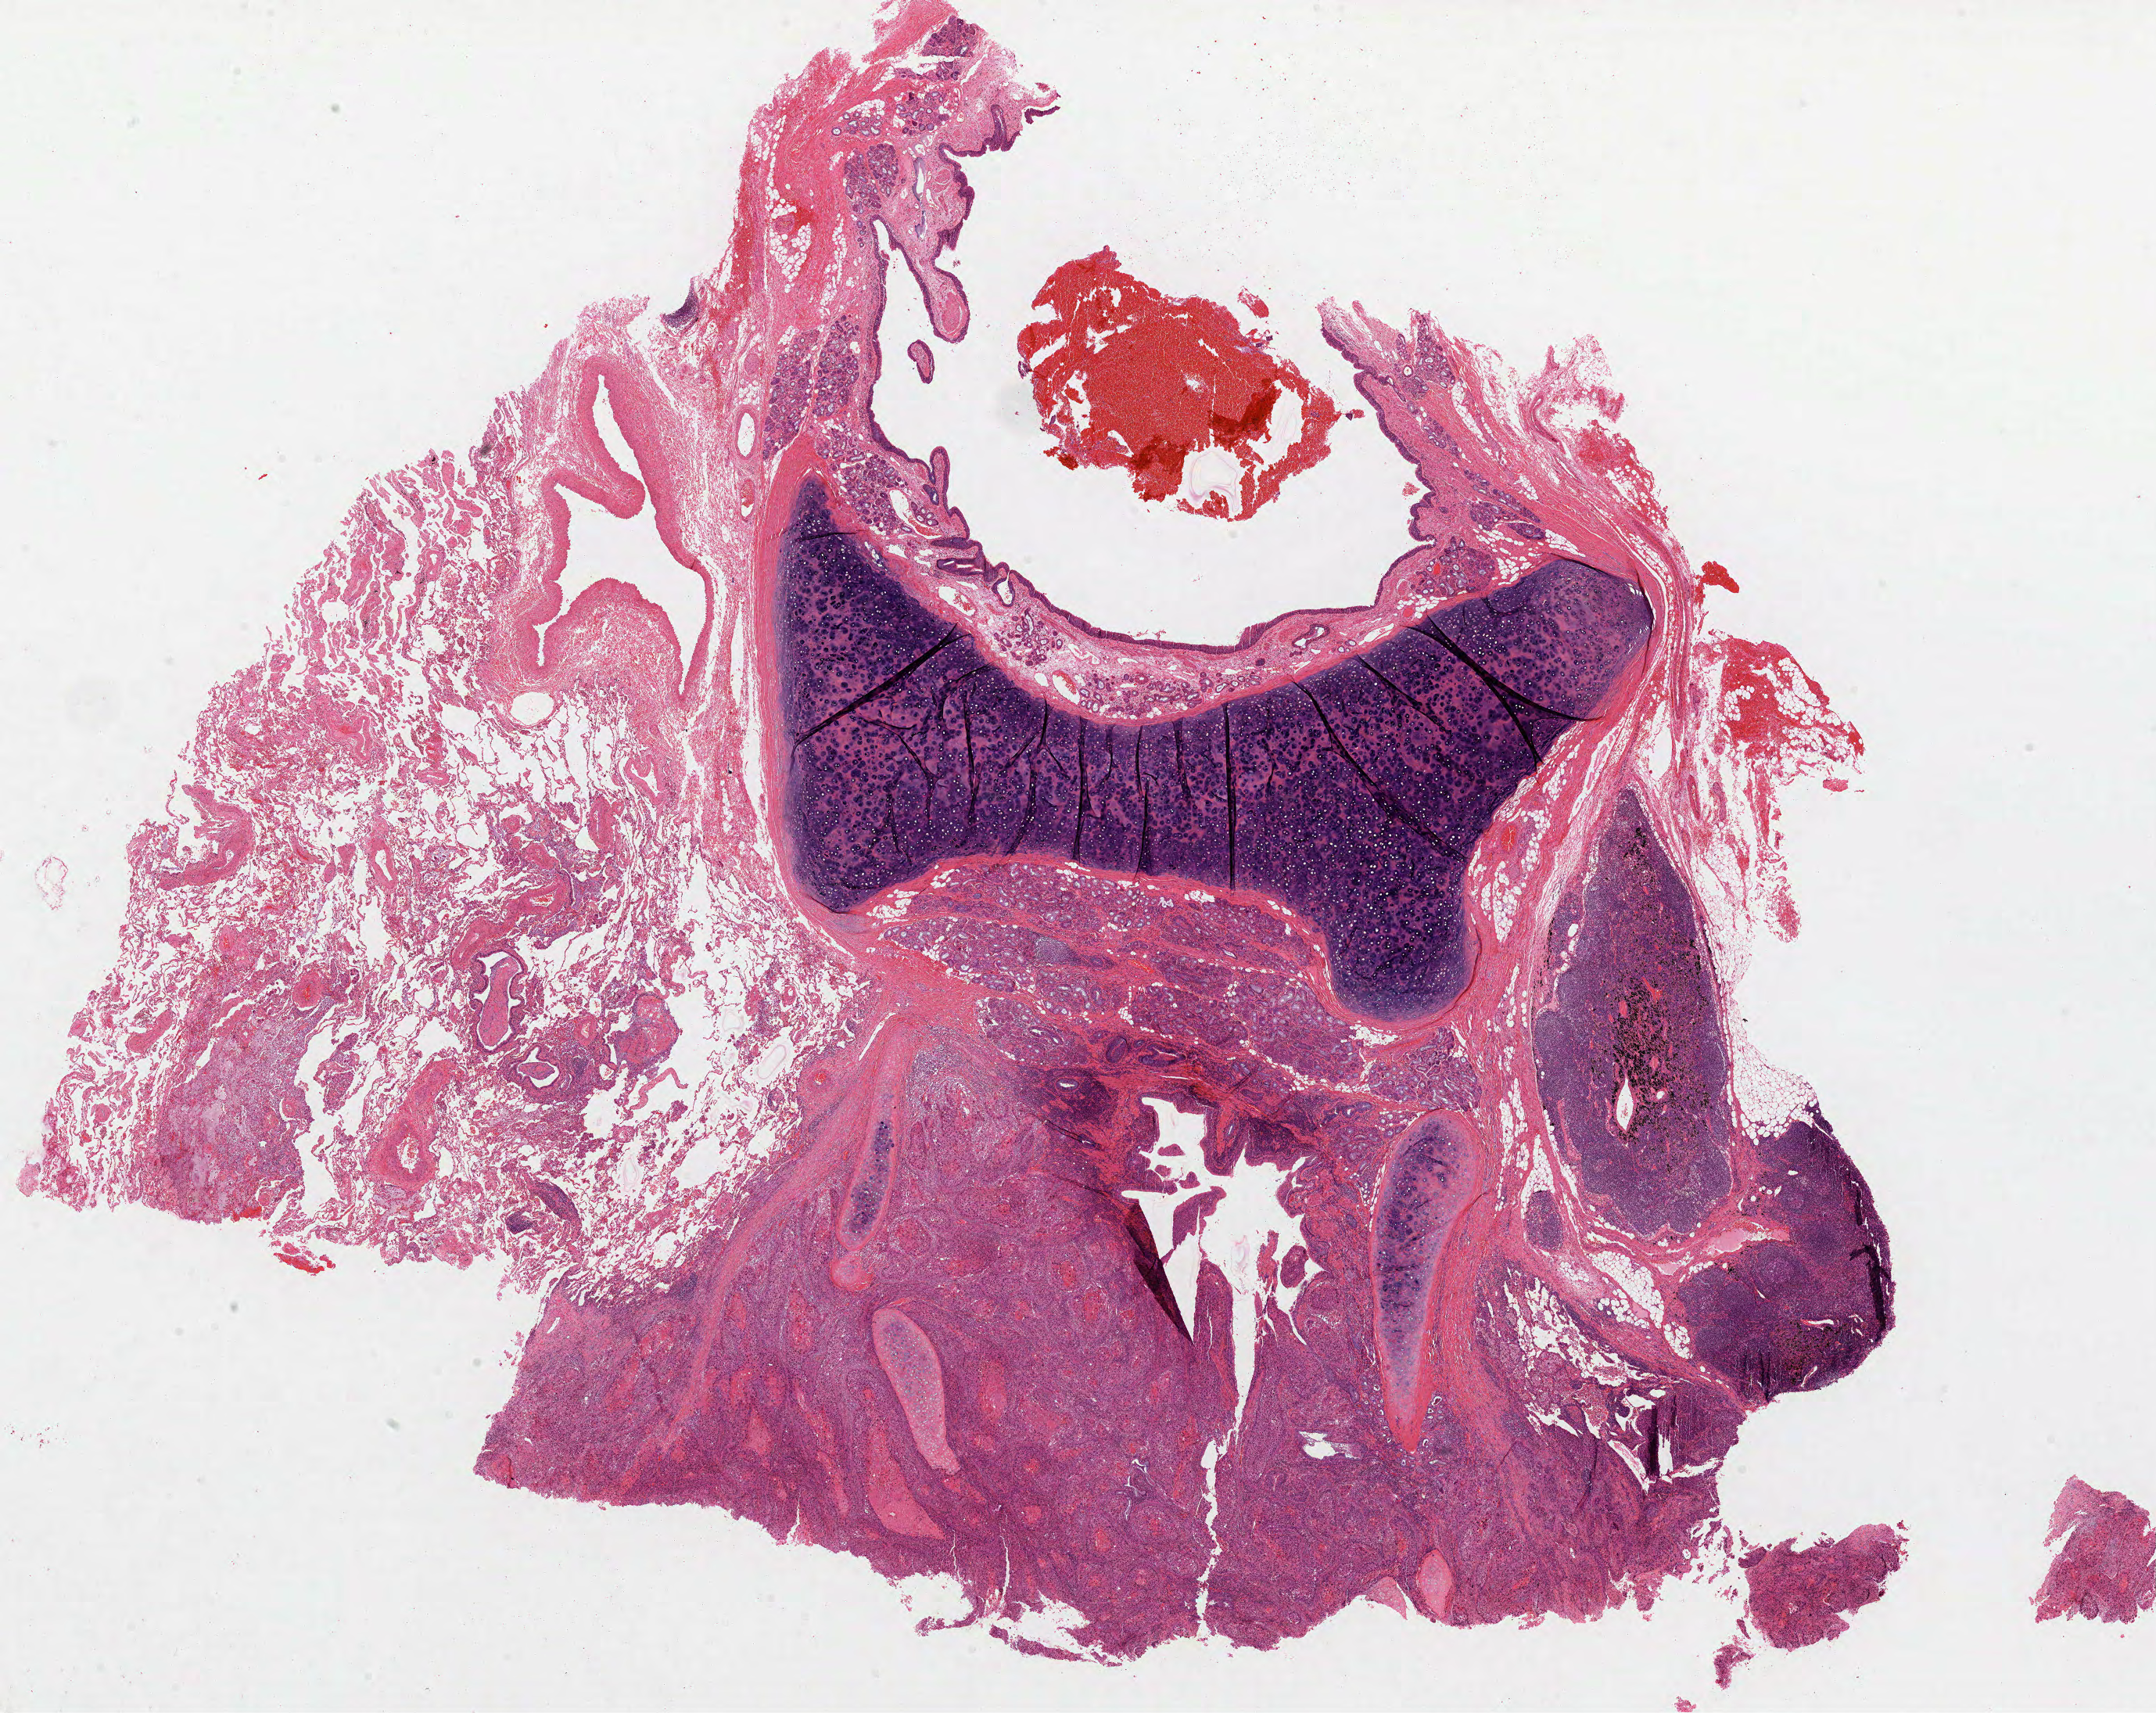
Digitized H&E tissue section (whole slide), a low-resolution overview of the entire scanned area, about 22.2 x 17.7 mm. Formalin-fixed paraffin-embedded (FFPE) diagnostic section. Primary tumour sample from the lung. Male, age 71 years at initial diagnosis.
TNM: T2a N0 MX. Diagnosis: Squamous cell carcinoma, NOS (upper lobe, lung). AJCC pathologic stage: IB.